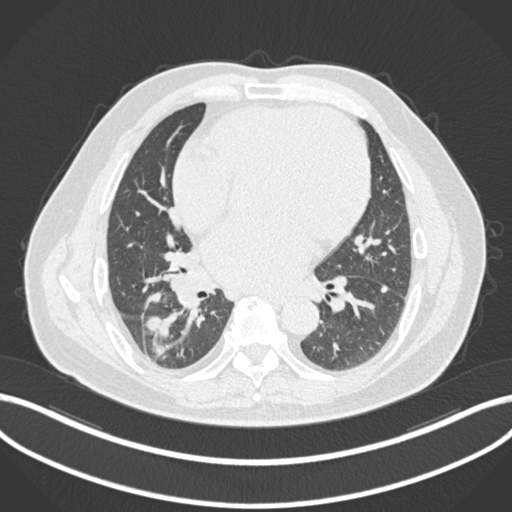
Chest CT, one axial slice. Slice 81 of 200 in the series (ordered by position). Reconstruction kernel B30f. Lung window (W 1500 / L -600 HU). 1 mm slice thickness. 512 × 512 image matrix. Patient: male, 59 years.
Structures marked on this image (bounding box drawn by a radiologist):
- lung tumour (recorded histology: adenocarcinoma): box from (x=144, y=284) to (x=176, y=358) px